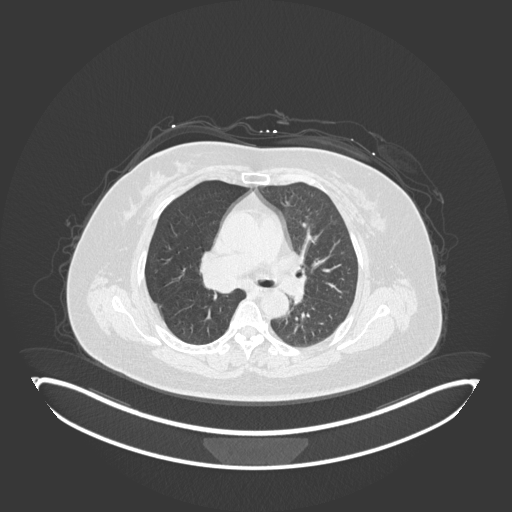
Chest CT, one axial slice; position 99 of 245 along the scan axis; lung window (W 1500 / L -600 HU); 1 mm slice thickness; 512 × 512 image matrix, field of view 500 × 500 mm. Patient: female, 60 years. From the clinical record (not read from this slice): clinical TNM (as recorded): T1c N0 M0; histopathological grade: G1-G2.
Annotated regions visible in this slice (rectangle marked by the reading radiologist):
- lung tumour (recorded histology: squamous cell carcinoma): bounding box [x1, y1, x2, y2] px = [203, 270, 242, 297]